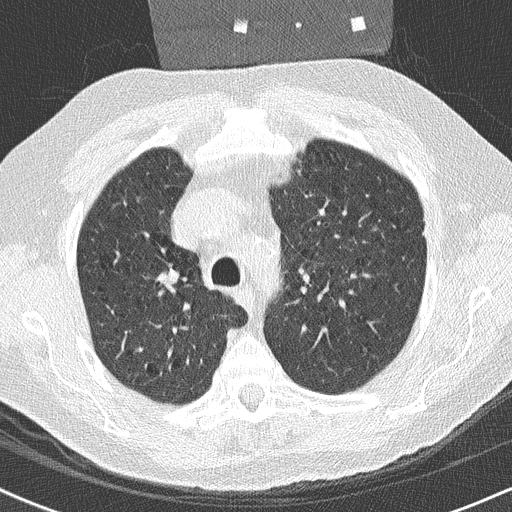
Chest CT (low-dose screening protocol), one axial image; baseline annual screen; lung window (W 1500 / L -600 HU); 2 mm slice thickness; lung (sharp) reconstruction kernel (B50f); 120 kVp; slice 79 of 250 in the series; 512 × 512 image matrix. Male participant, aged 59 years at enrolment. Former smoker at enrolment.
Expert-annotated lung lesion, bounding box <146,260,187,299> (left, top, right, bottom; pixels). No non-calcified nodule or mass ≥4 mm was recorded by the screening reader at this exam. Lung cancer was diagnosed 360 days after this screen (after the second annual screen): squamous cell carcinoma, NOS, right upper lobe, poorly differentiated (G3), stage IIA (AJCC 6th edition), 20 mm at pathology.